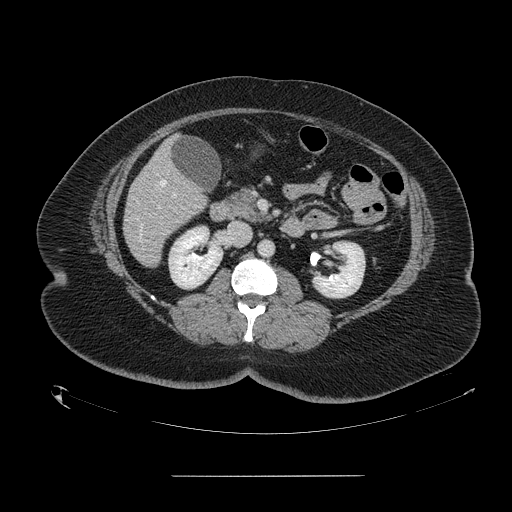
Contrast-enhanced abdominal CT, one axial slice. Position 60 of 164 along the scan axis. Soft-tissue window (W 400 / L 40 HU). 2.5 mm slice thickness. 512 × 512 image matrix. Female patient, age 52 years. Case-level facts recorded for this patient, not image findings: diagnosis: colorectal cancer liver metastases, imaged before liver resection; multiple liver metastases: yes; largest metastasis: 3.5 cm; chemotherapy before resection: no.
Annotated regions visible in this slice (outlined manually by an expert reader):
- hepatic veins: bounding box <136,180,166,242> (left, top, right, bottom; pixels)
- liver: <124,142,207,266>
- portal vein (with intrahepatic branches): <172,194,176,197>